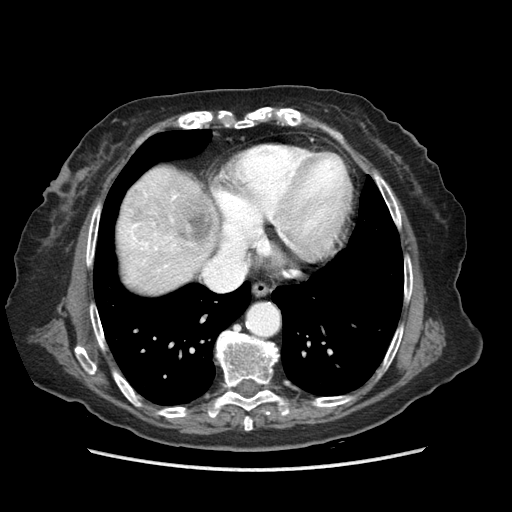
Contrast-enhanced abdominal CT (liver protocol), one axial slice. Position 77 of 89 along the scan axis. Reconstruction kernel STANDARD. Soft-tissue window (W 400 / L 40 HU). 512 × 512 image matrix, field of view 360 × 360 mm. From the clinical record (not read from this slice): diagnosis: hepatocellular carcinoma (patient treated with transarterial chemoembolisation; whether this scan precedes or follows treatment is not stated here); TNM stage (as recorded): Stage-IIIA; Child-Pugh class: A; tumour differentiation: well differentiated; tumour nodularity: multinodular.
Outlined on this slice (semi-automatic segmentation, software-assisted and operator-edited):
- liver parenchyma outside the tumour (the mass and vessels are separate outlines, so this box may not span the whole liver): bounding box <116,166,220,294> (left, top, right, bottom; pixels)
- mass: <172,210,213,242>
- liver vessels: <127,195,177,271>